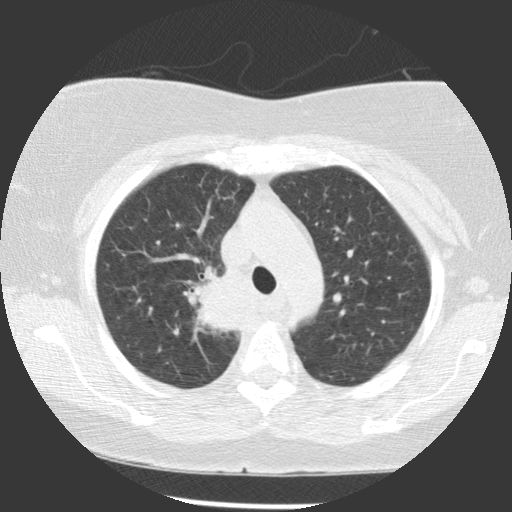
Low-dose screening chest CT, axial slice. Baseline annual screen. Lung window (W 1500 / L -600 HU). 2.5 mm slice thickness. Slice 86 of 116 in the series. 512 × 512 image matrix. Female participant, aged 63 years at enrolment. Former smoker at enrolment.
Expert reader's lesion annotation, bounding box [x1, y1, x2, y2] px = [194, 264, 254, 325]. The exam's reader record, not a measurement of the box and not confirmed to be the same lesion: non-calcified nodule or mass ≥4 mm, right upper lobe, 39 × 36 mm, spiculated (stellate) margins, soft tissue attenuation. Official screen result: positive, change unspecified: nodule(s) >= 4 mm or enlarging nodule(s), mass(es), or other non-specific abnormalities suspicious for lung cancer. Participant outcome: lung cancer diagnosed 72 days after this screen — non-small cell carcinoma, right upper lobe, carina, right main stem bronchus, poorly differentiated (G3), stage IIIA (AJCC 6th edition), 66 mm at pathology.